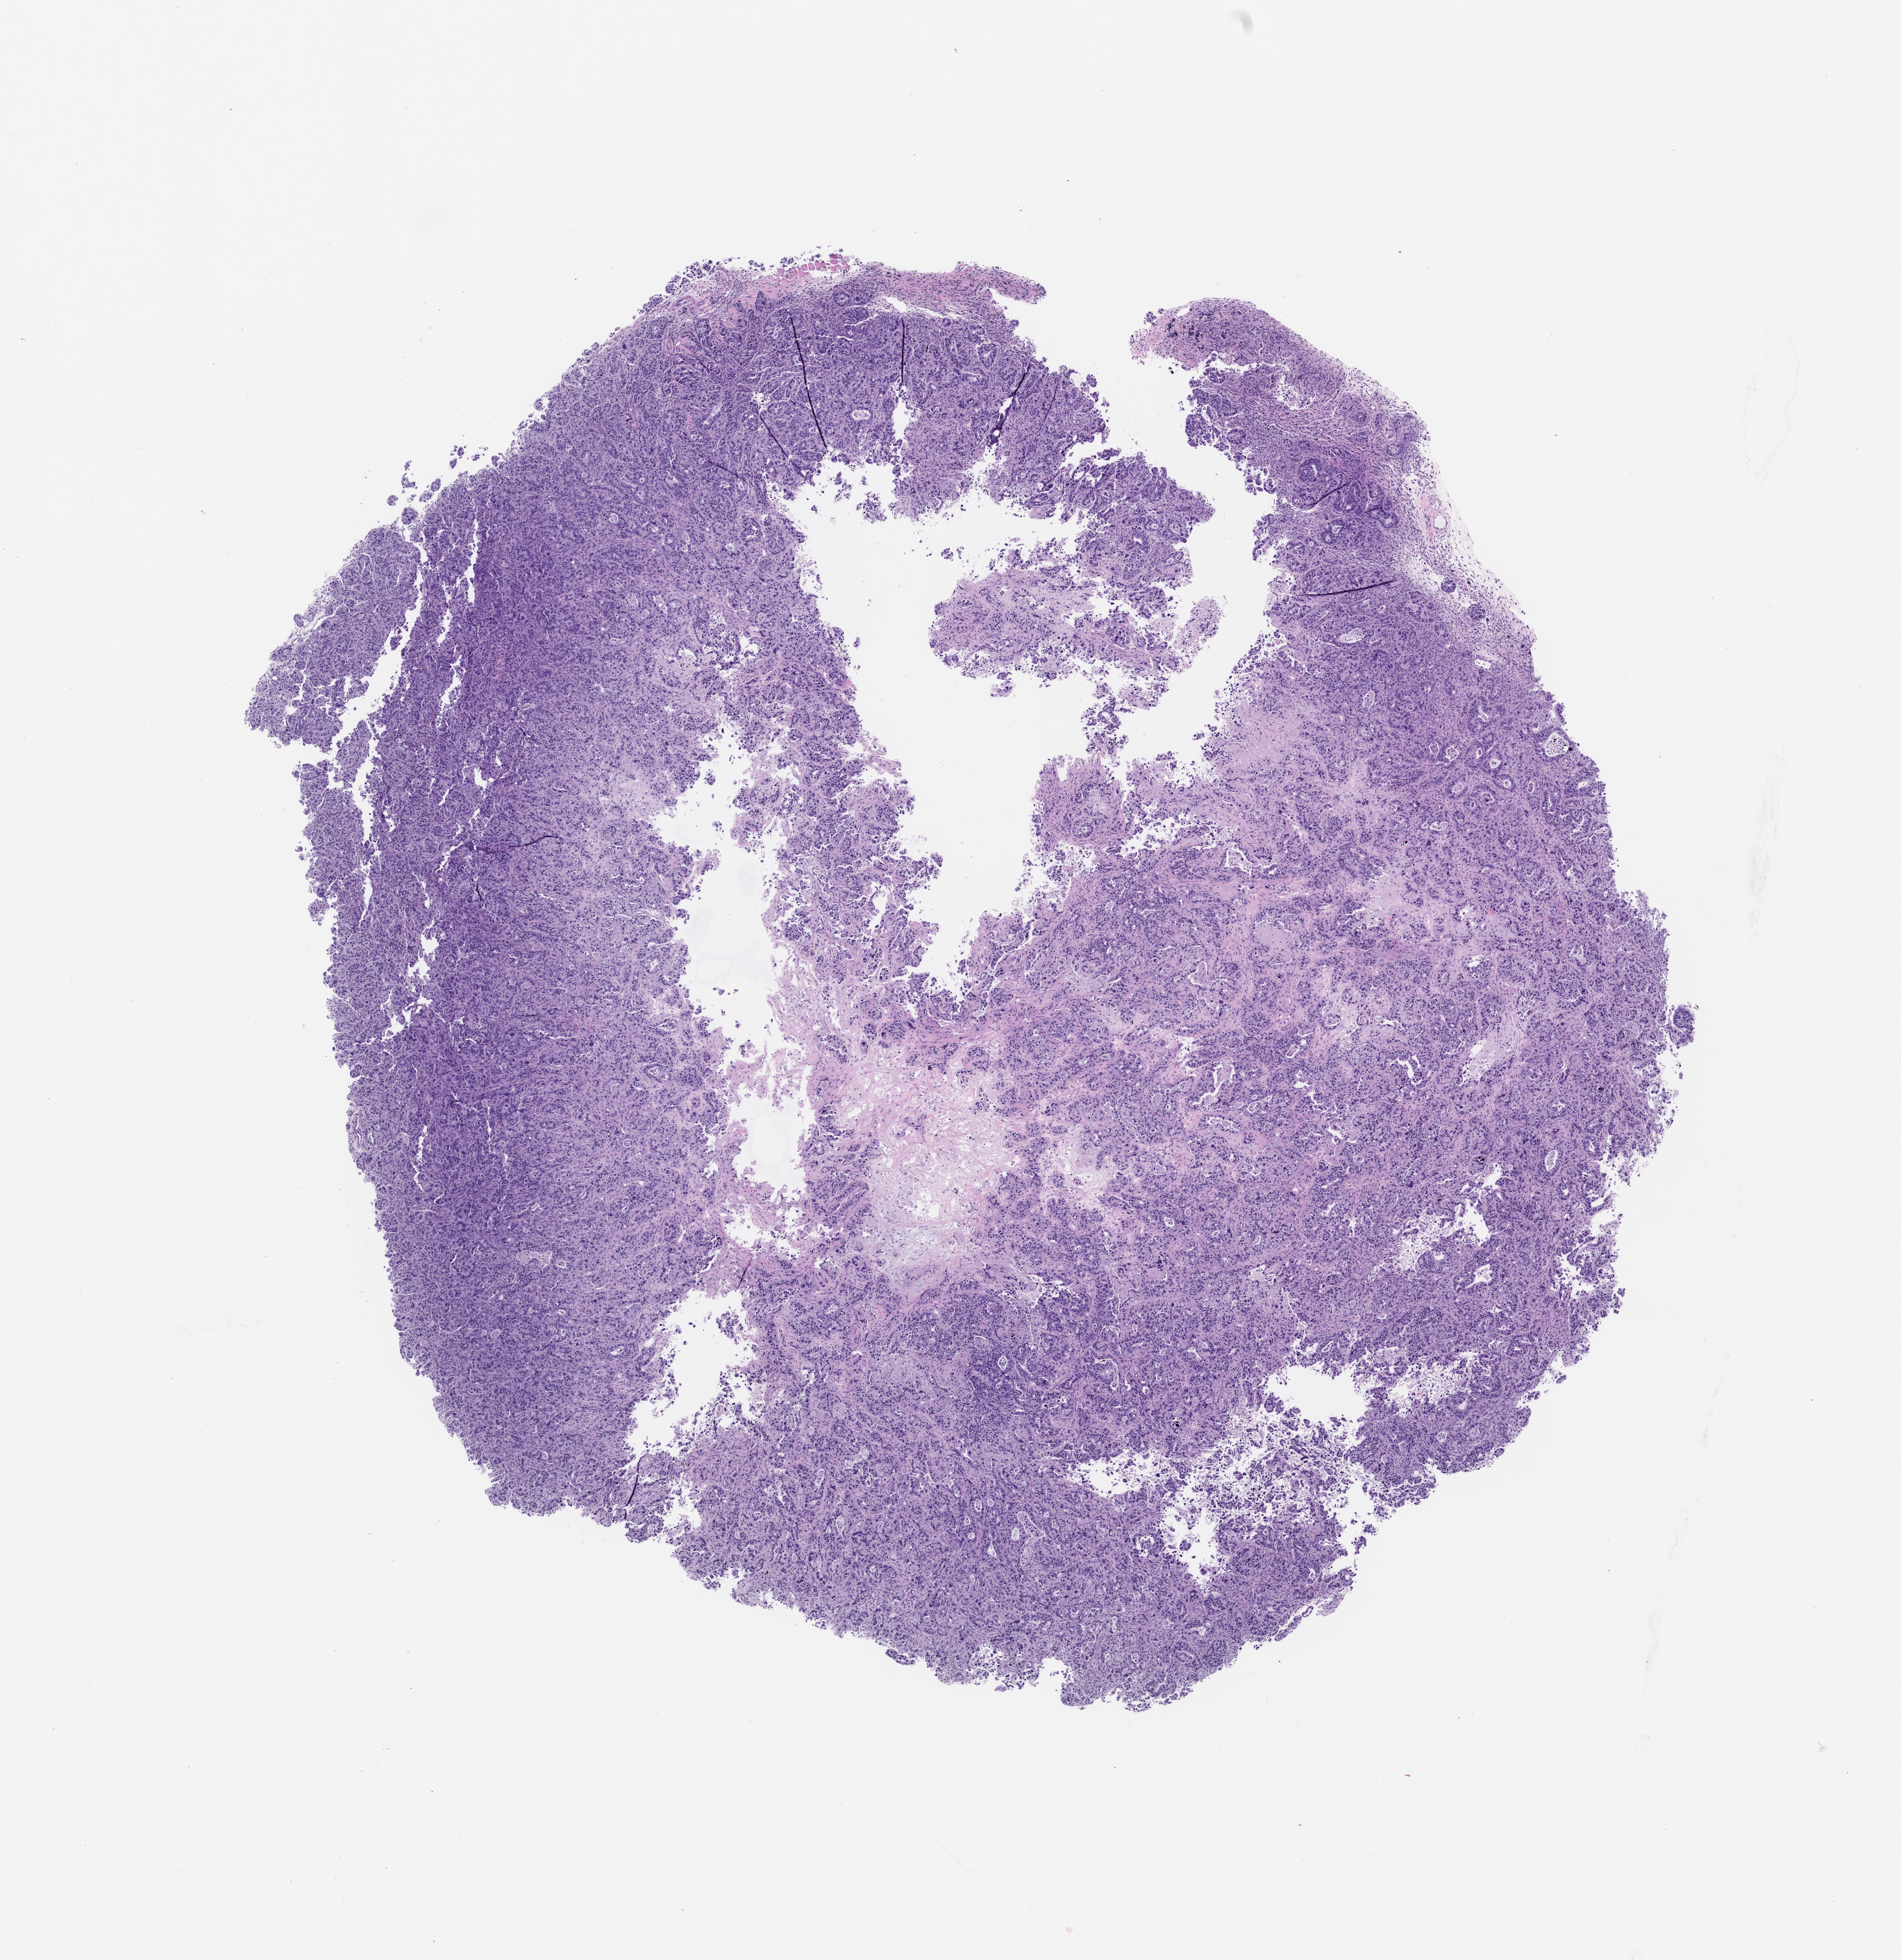
Haematoxylin and eosin whole-slide image of a patient-derived xenograft (PDX) tumor grown in a mouse, passage 2, a low-resolution overview of the entire scanned area, about 11.0 x 11.3 mm; FFPE section; tumor site category: pancreas.
Originating patient diagnosis: Pancreatic Adenocarcinoma.